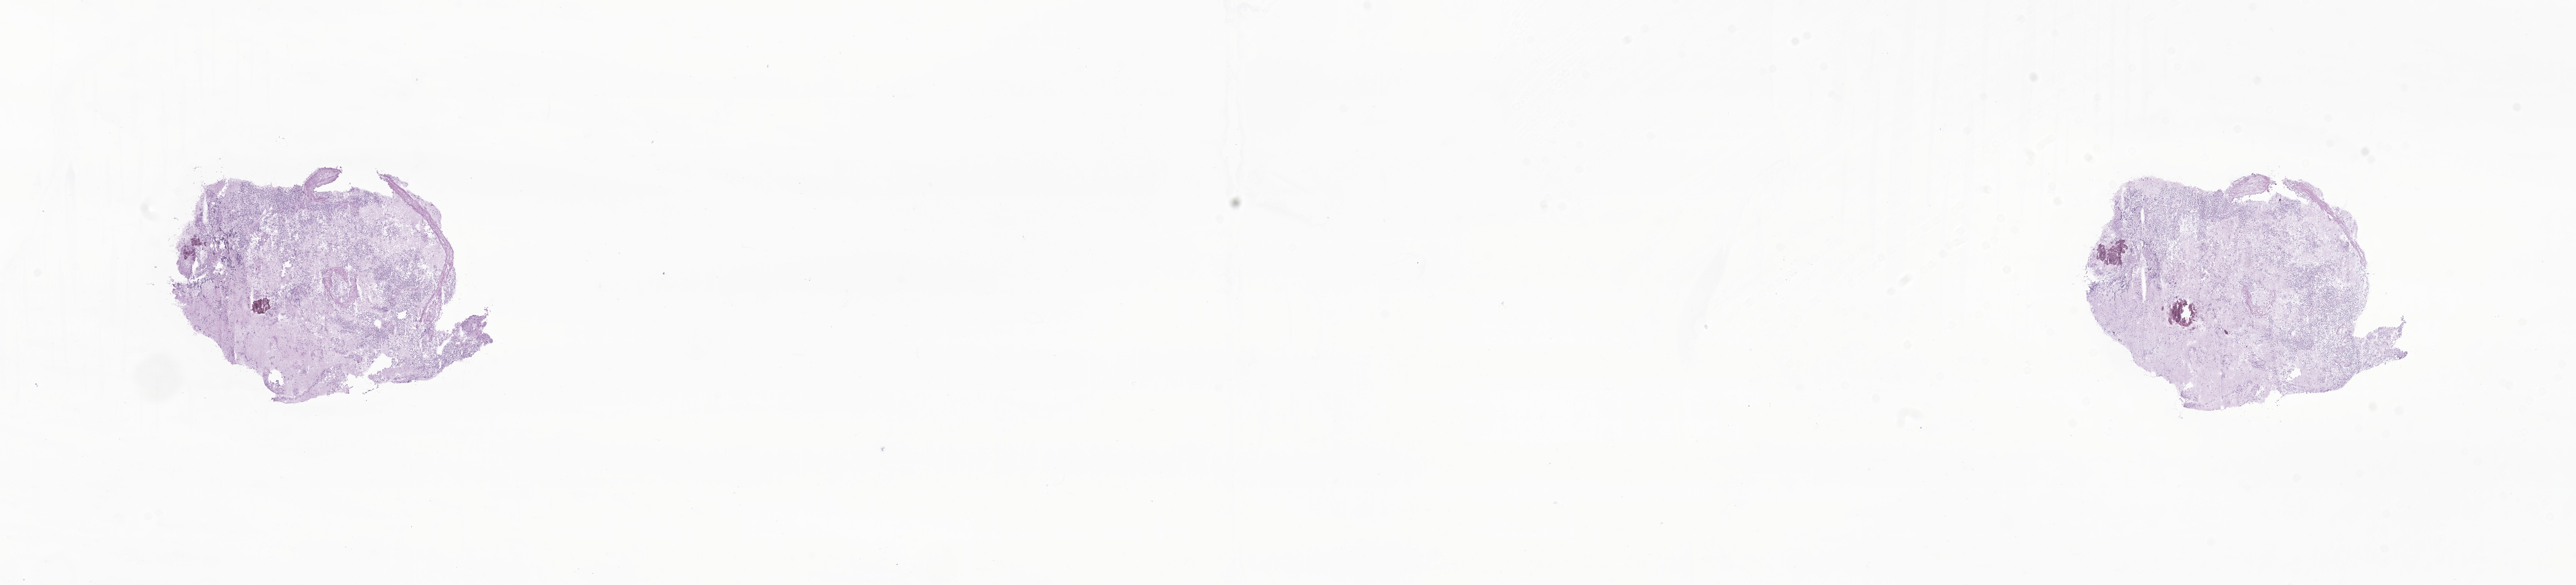
H&E whole-slide image of tumor tissue from the brain — whole scanned area (about 28.2 x 6.4 mm) shown as a low-resolution overview, frozen section. Patient female; age 69 months (5 years 9 months).
- recorded diagnosis: Medulloblastoma, NOS